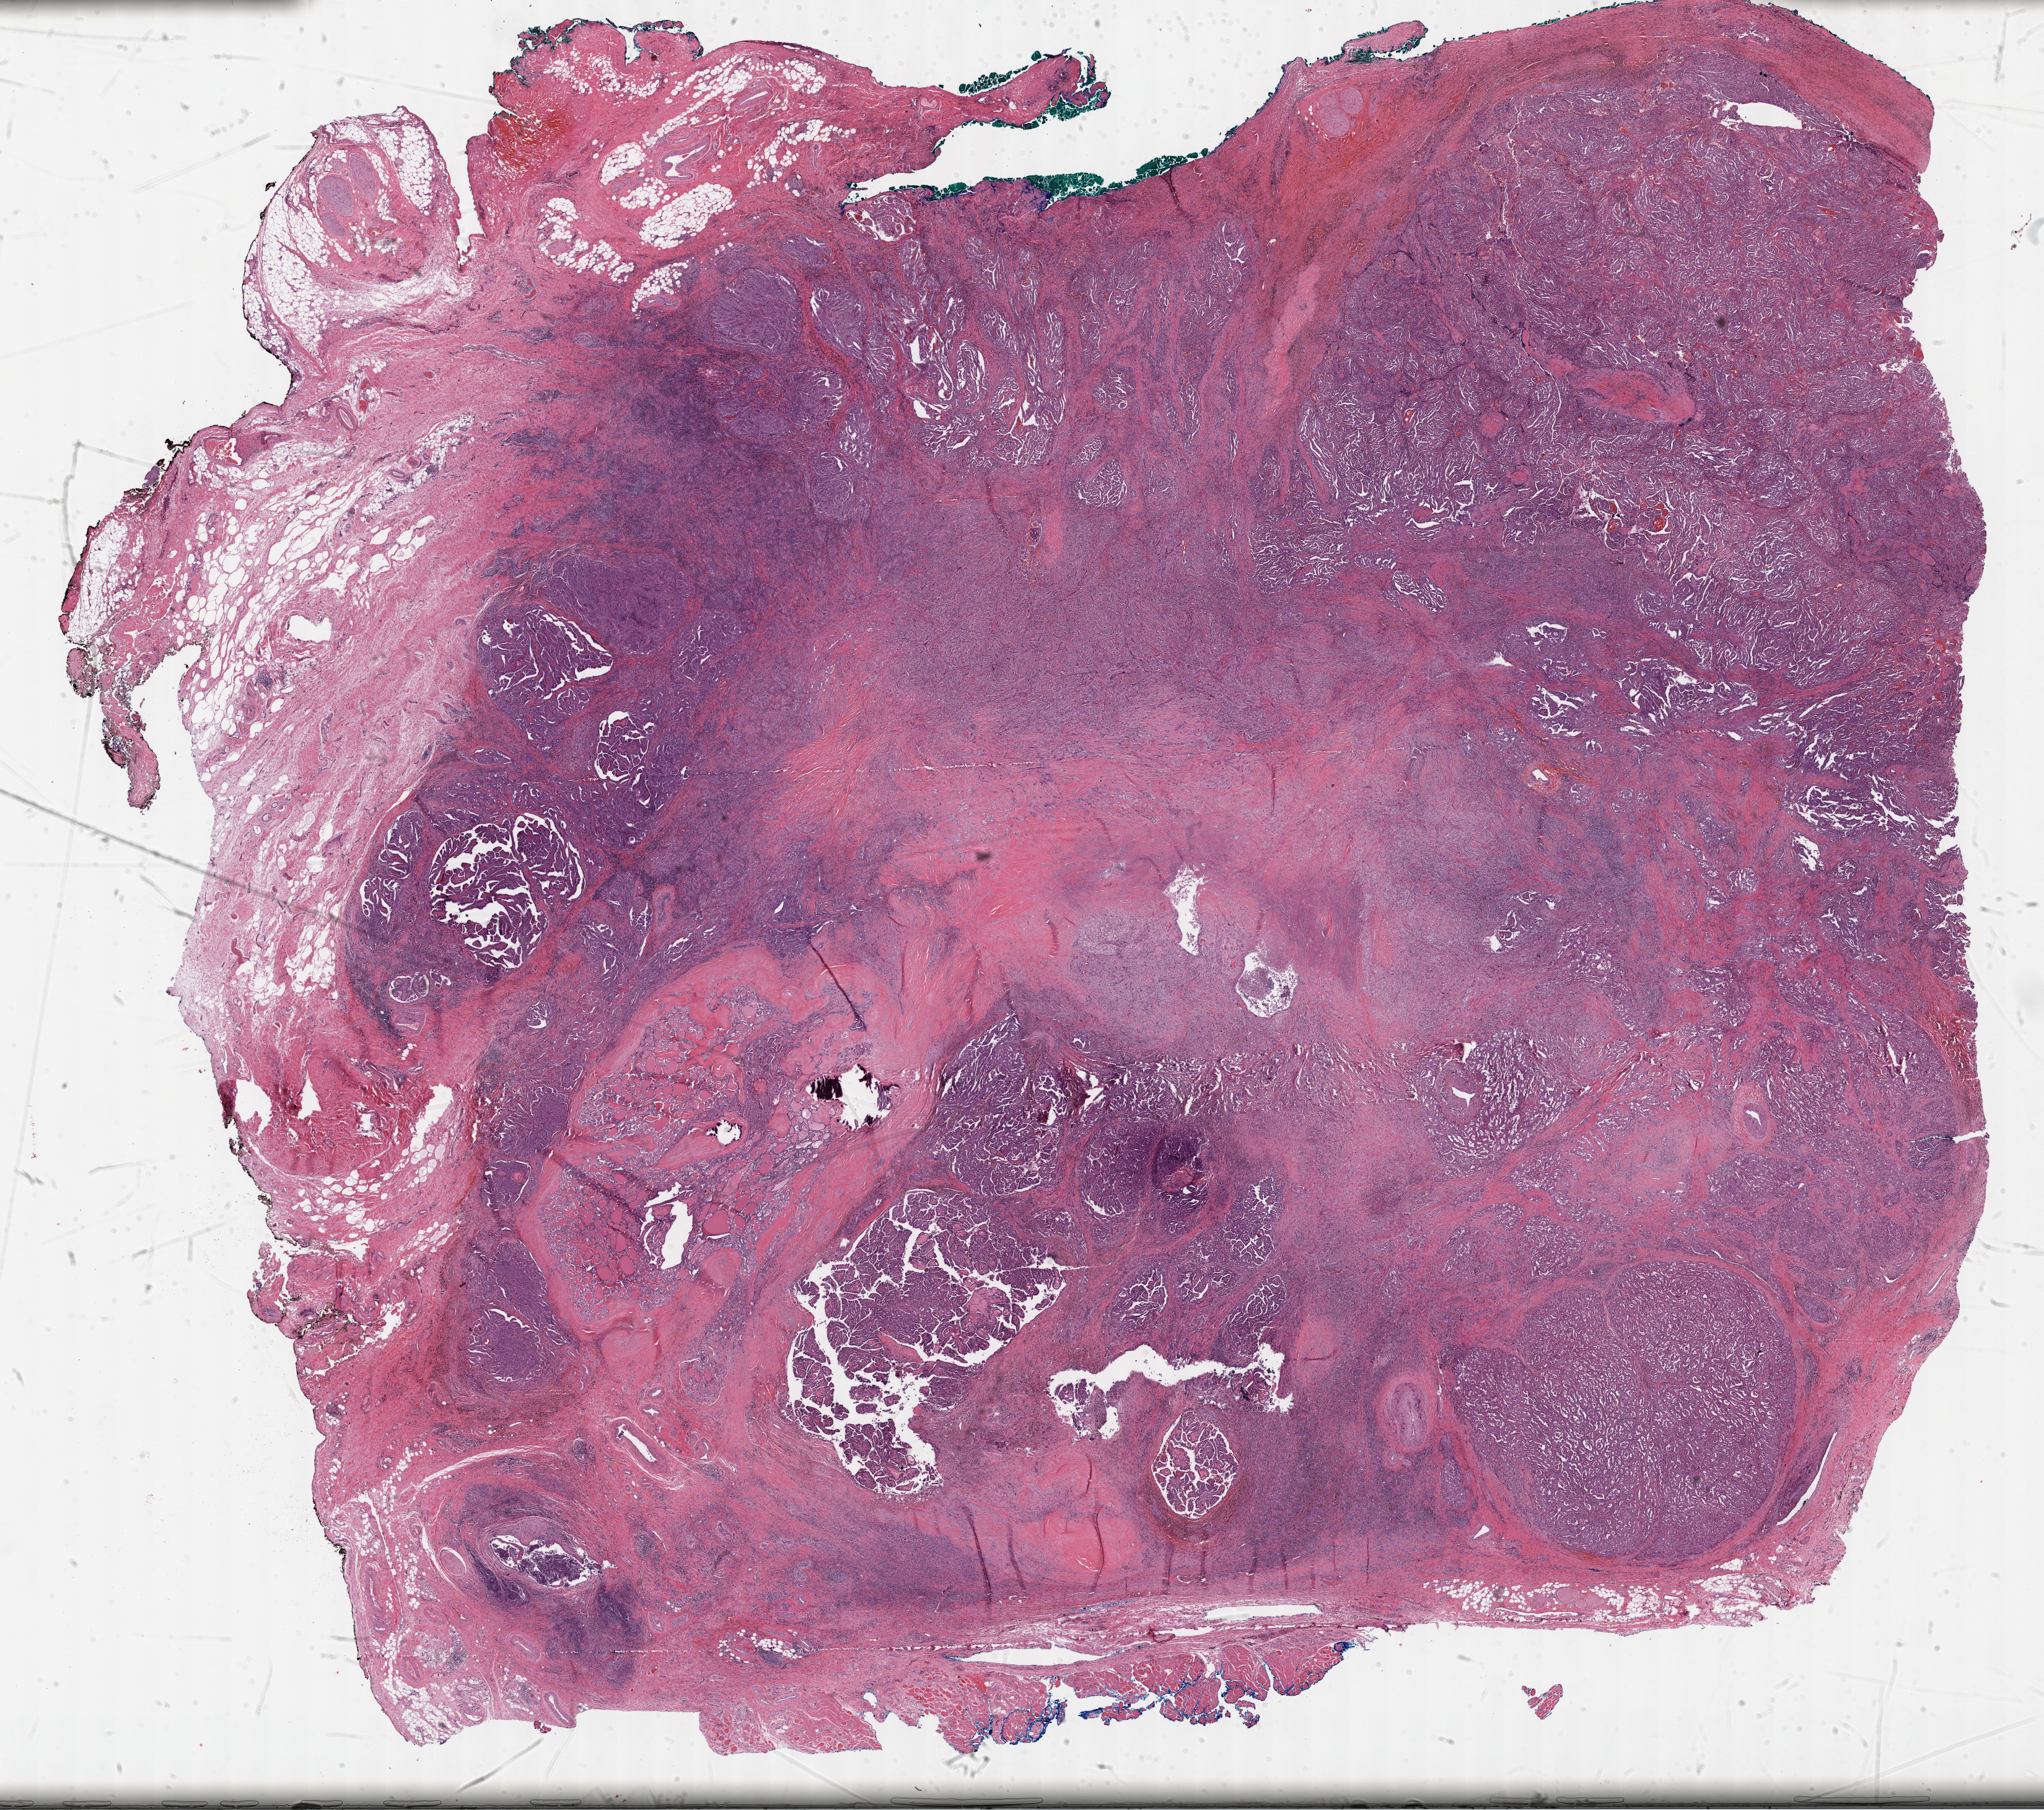
H&E-stained whole-slide image, a low-resolution overview of the entire scanned area, about 26.7 x 23.6 mm (acquisition: 40x scan); formalin-fixed paraffin-embedded (FFPE) diagnostic section; primary tumour sample from the thyroid. Female, age 74 years at initial diagnosis.
* lymph nodes positive (case pathology): 1 of 41 examined
* laterality: right
* pathologic diagnosis: Papillary carcinoma, NOS
* AJCC pathologic stage: IVA (7th edition)